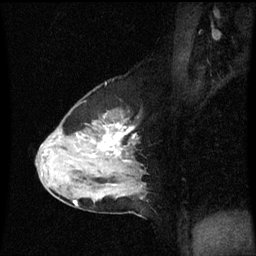
Breast MRI (dynamic contrast-enhanced), one sagittal slice; position 40 of 60 along the scan axis; dynamic contrast-enhanced series, image 2 of 3 at this slice position (ordered by acquisition); 1.5 T; TE 4.2 ms, TR 8.9 ms; 256 × 256 image matrix. Female patient, age 50 years. Case-level facts recorded for this patient, not image findings: setting: breast cancer imaged before/during neoadjuvant chemotherapy; receptor status: HR-positive, HER2-negative.
Annotated regions visible in this slice (semi-automatic segmentation, software-assisted and operator-edited):
- analysis volume of interest (the breast-tissue region the enhancement analysis was run in; not a lesion): bounding box (x1, y1, x2, y2) in pixels: (38, 110, 148, 209)
- tumour enhancement mask (voxels above the 70 % enhancement threshold inside the analysis volume of interest): (84, 132, 122, 155)